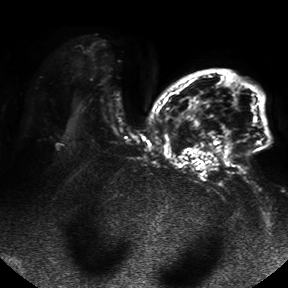
Breast MRI, one axial slice. Position 29 of 50 along the scan axis. Diffusion-weighted series; image 2 of 4 stored at this slice position (different b-values; order by instance number). 1.5 T. 4 mm slice thickness. 288 × 288 image matrix, field of view 390 × 390 mm. Female patient.
Structures marked on this image (outlined manually by an expert reader):
- tumour on diffusion-weighted imaging: box from (x=175, y=104) to (x=234, y=152) px